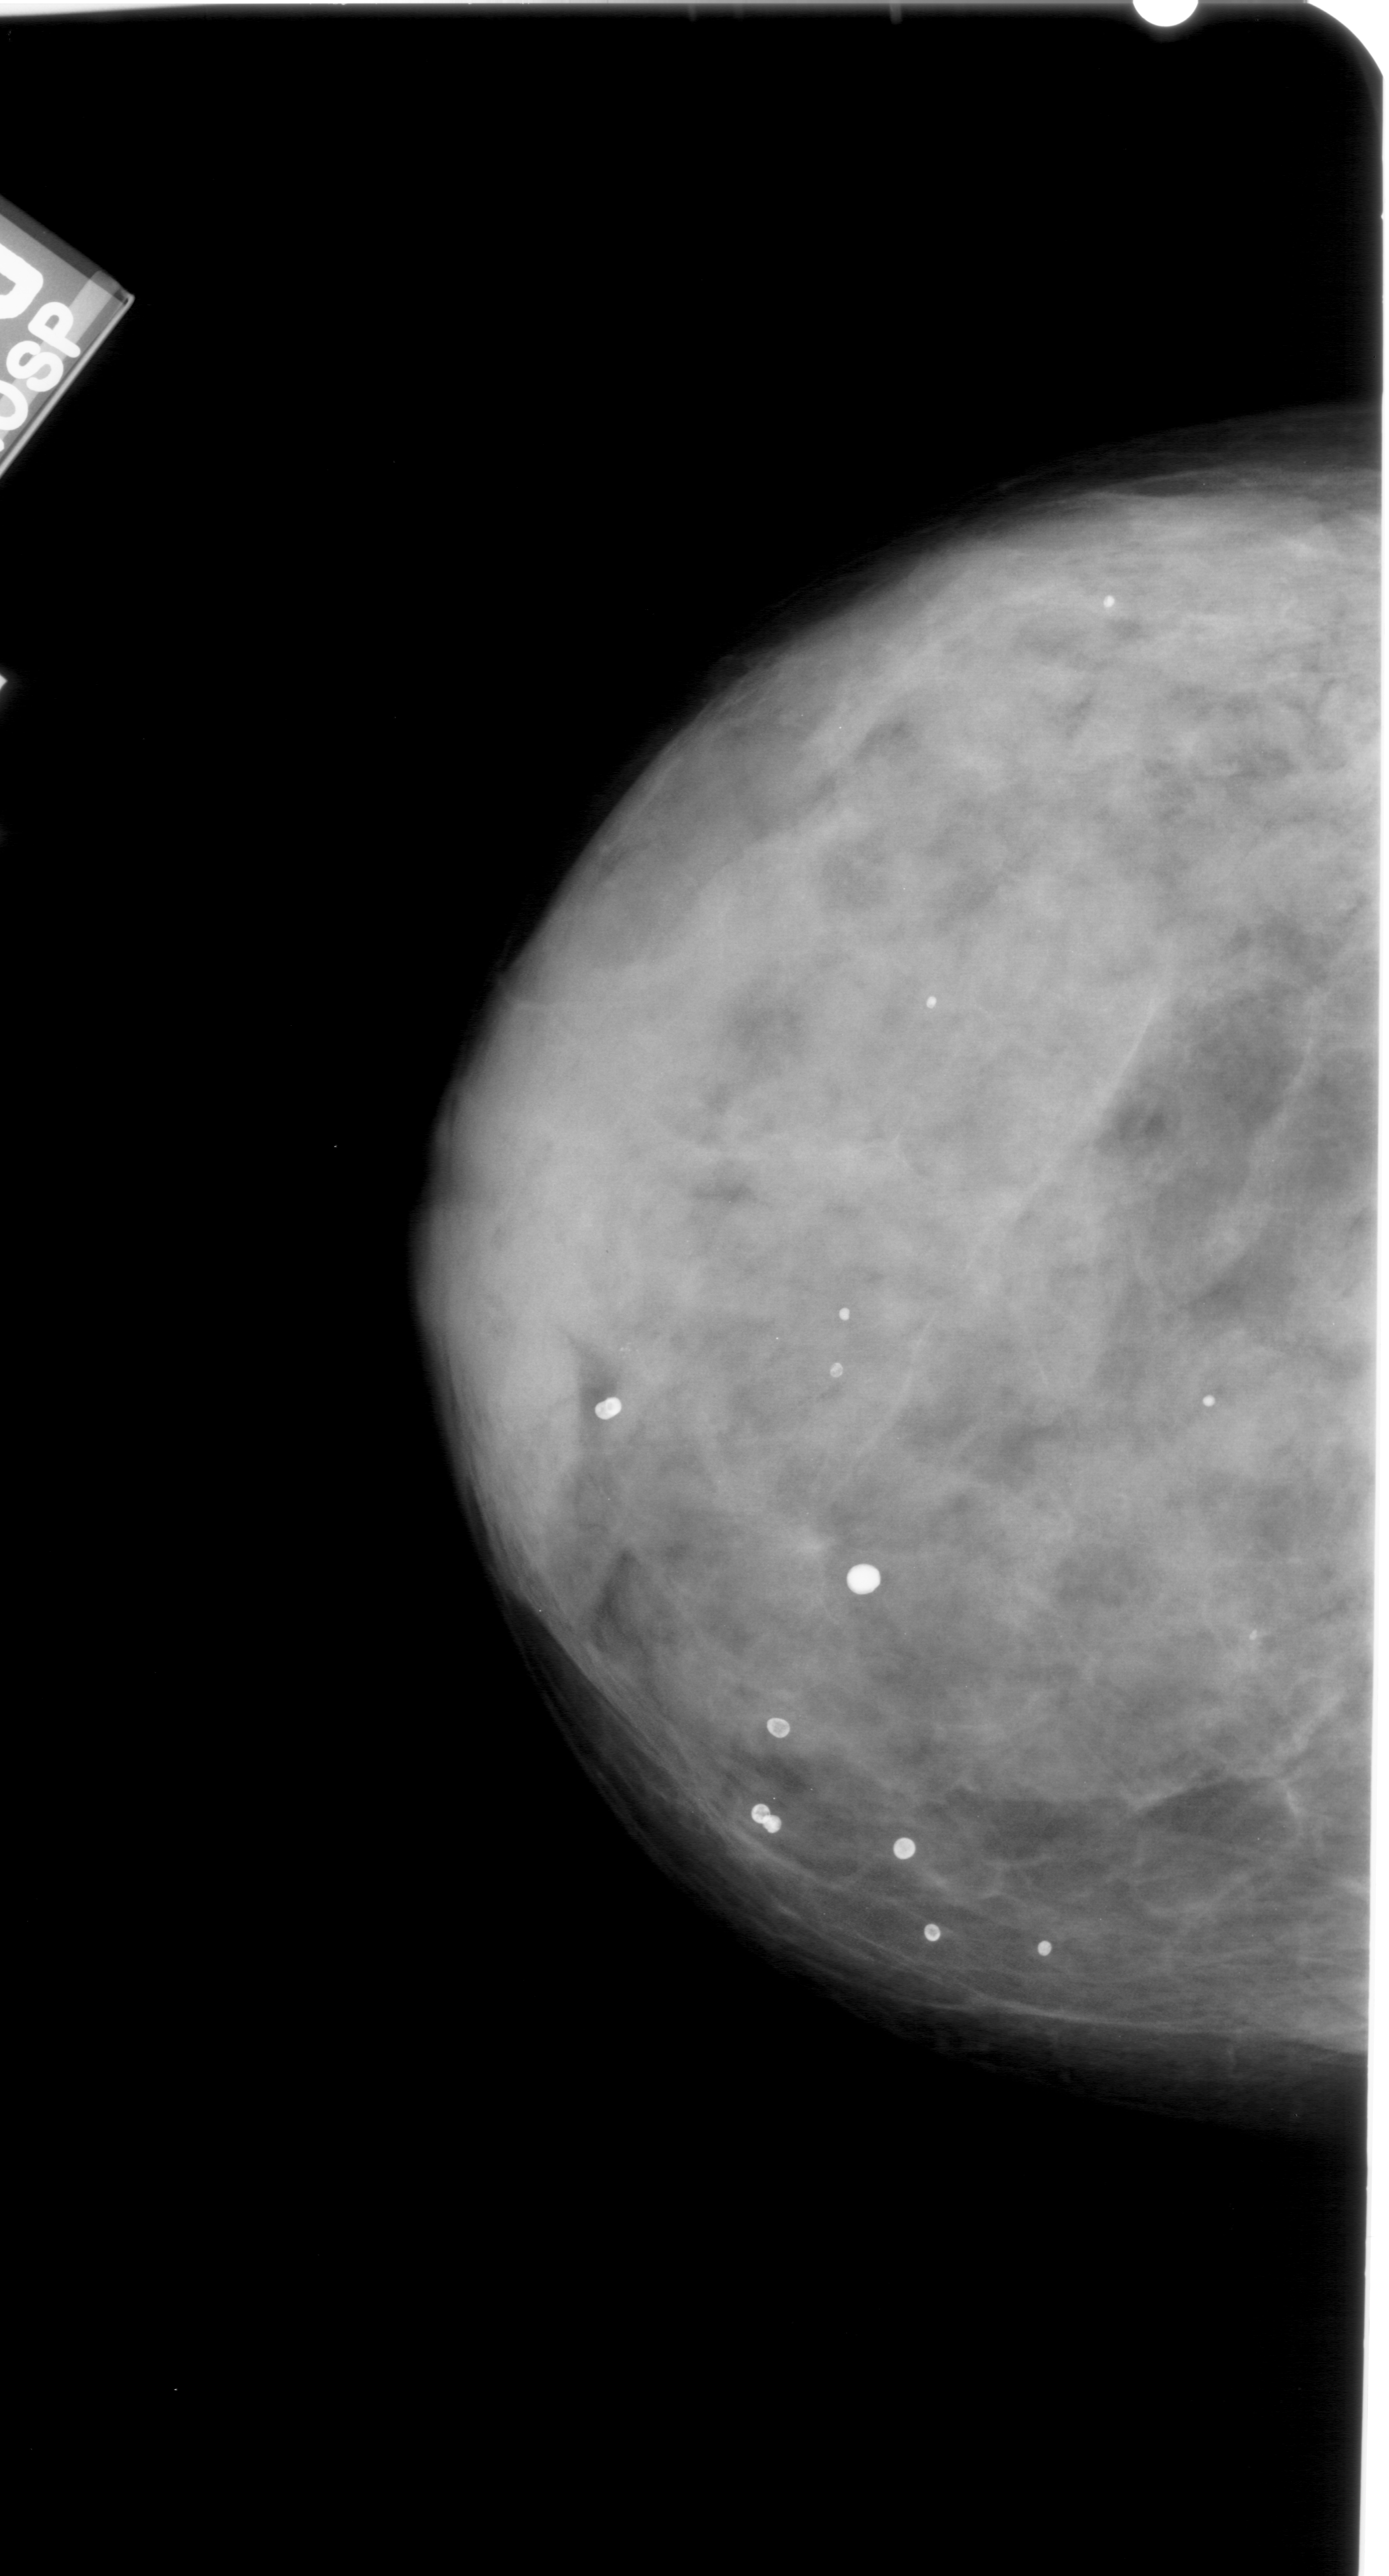
Digitized screen-film mammogram; left breast; CC view; breast composition: extremely dense (BI-RADS density category 4 of 4).
Marked abnormality: calcifications, morphology amorphous, distribution clustered; BI-RADS assessment category 4; subtlety rating 2 on a 1 (subtle) to 5 (obvious) scale; pathology (as recorded): benign.